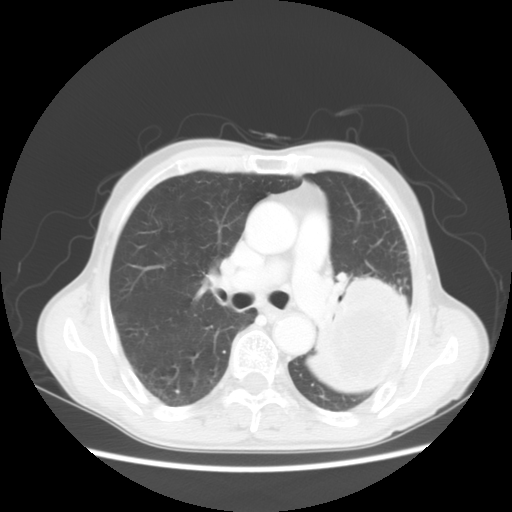
Chest CT, one axial slice. Slice 31 of 51 in the series (ordered by position). Reconstruction kernel STANDARD. Lung window (W 1500 / L -600 HU). 5 mm slice thickness. 512 × 512 image matrix. Male patient, age 64 years. Case-level facts recorded for this patient, not image findings: clinical TNM (as recorded): T4 N0 M0; histopathological grade: G2-3.
Annotated regions visible in this slice (rectangle marked by the reading radiologist):
- lung tumour (recorded histology: squamous cell carcinoma): bounding box [x1, y1, x2, y2] px = [307, 269, 404, 394]